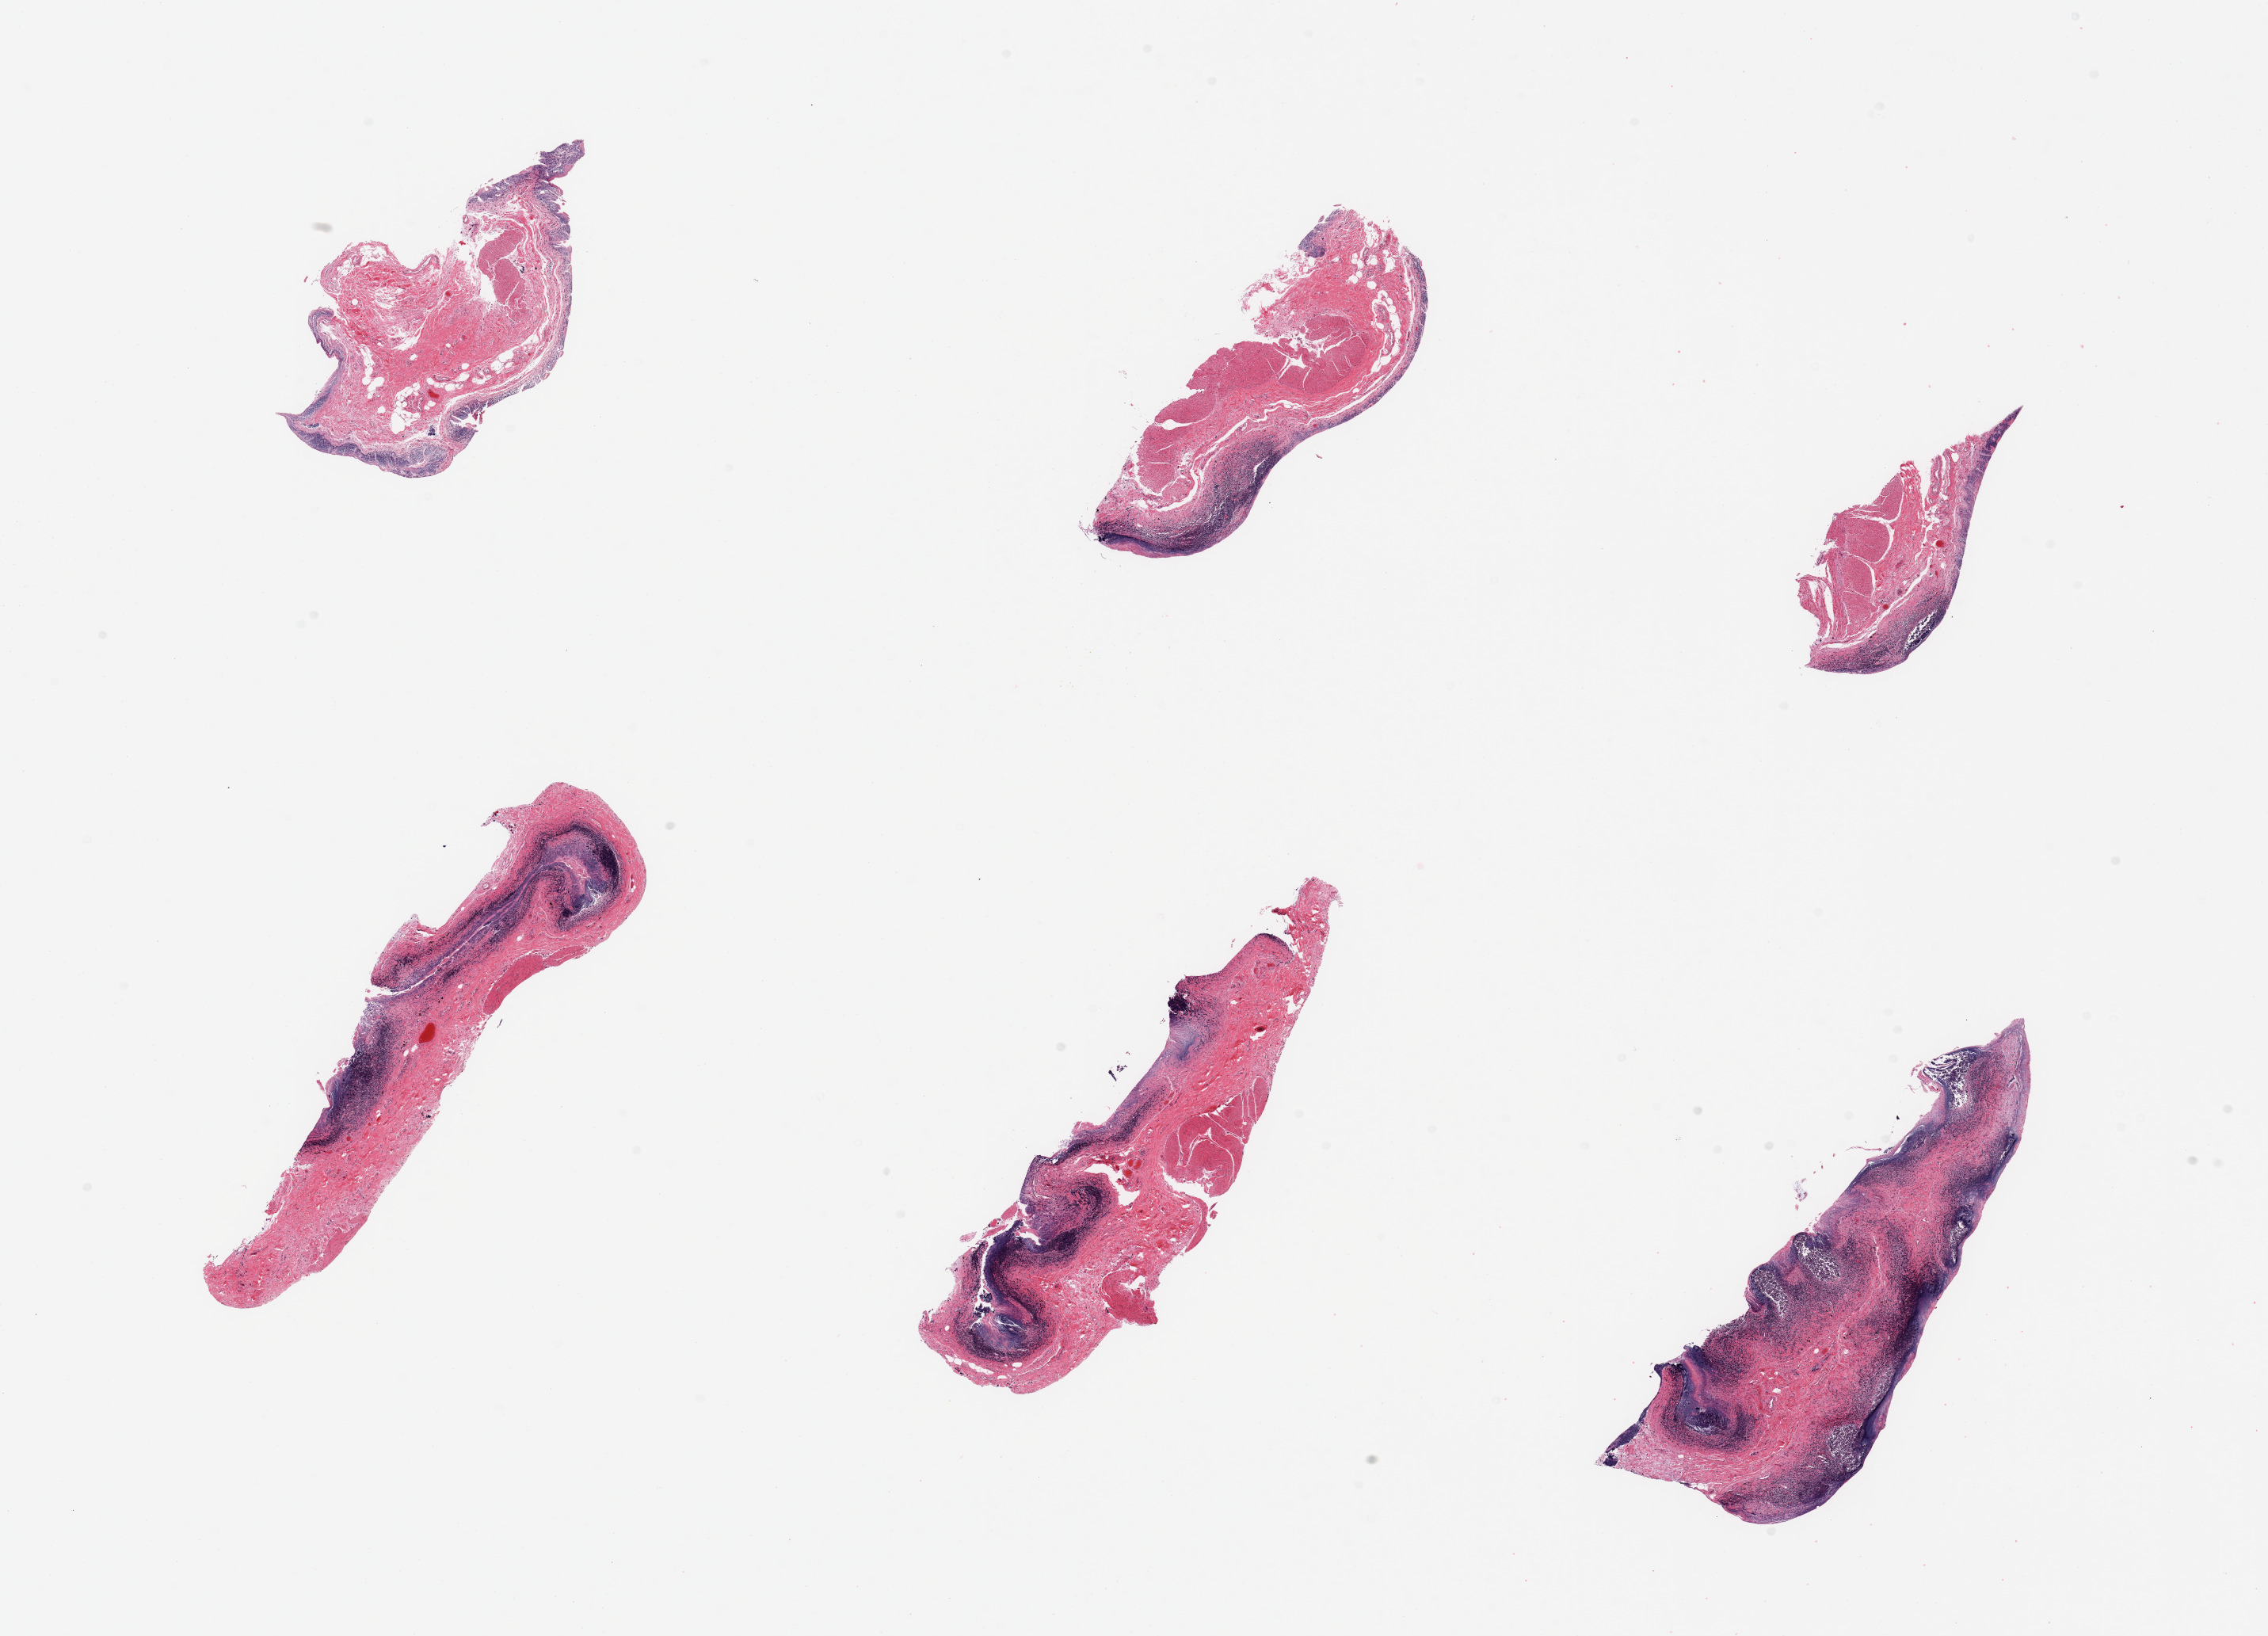
Whole-slide image, haematoxylin and eosin stain — shown as a low-resolution overview of the whole scanned area (about 22.6 x 16.3 mm, slide scanned at 20x); PAXgene-fixed, paraffin-embedded tissue; target tissue: ileum; donor tissue sample.
Pathologist's review note for this sample: 6 pieces; autolyzed mucosa with some dispersed residual lymphoid component, muscularis also present (not target).